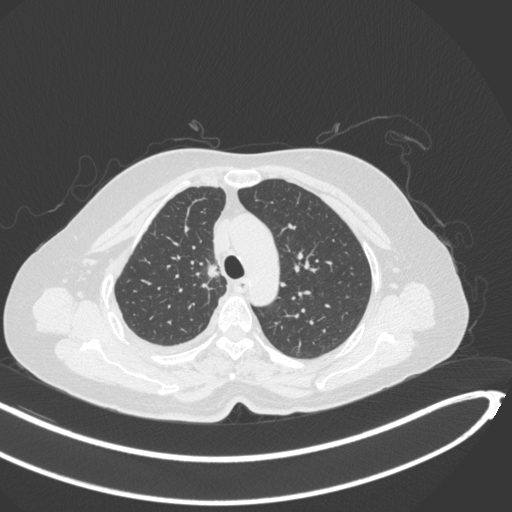
Chest CT, one axial slice. Slice 228 of 297 in the series (ordered by position). Reconstruction kernel B31f. 120 kVp. Lung window (W 1500 / L -600 HU). 1 mm slice thickness. 512 × 512 image matrix, field of view 400 × 400 mm. Patient: female, 64 years. Case-level facts recorded for this patient, not image findings: clinical TNM (as recorded): T1b N0 M1.
Annotated regions visible in this slice (rectangle marked by the reading radiologist):
- lung tumour (recorded histology: adenocarcinoma): bounding box (x1, y1, x2, y2) in pixels: (198, 257, 223, 285)